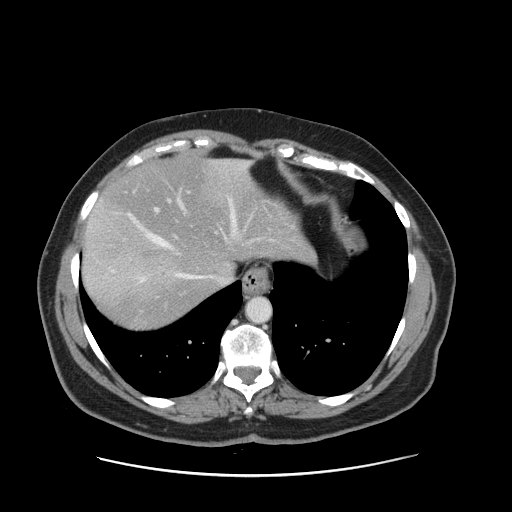
Contrast-enhanced abdominal CT, one axial slice; position 127 of 161 along the scan axis; intravenous contrast given; soft-tissue window (W 400 / L 40 HU); 512 × 512 image matrix, field of view 398 × 398 mm. Female patient, age 62 years. From the clinical record (not read from this slice): diagnosis: colorectal cancer liver metastases, imaged before liver resection.
Outlined on this slice (outlined manually by an expert reader):
- hepatic veins: bounding box (x1, y1, x2, y2) in pixels: (110, 162, 249, 283)
- liver: (82, 160, 303, 328)
- planned liver remnant (the part of the liver to remain after resection): (94, 160, 304, 279)
- portal vein (with intrahepatic branches): (155, 191, 190, 239)